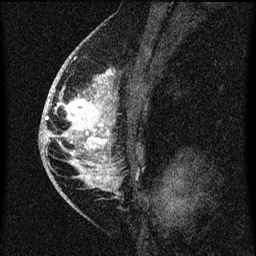
Breast MRI (dynamic contrast-enhanced), one sagittal slice; slice 39 of 60 in the series (ordered by position); dynamic contrast-enhanced series, image 2 of 3 at this slice position (ordered by acquisition); 1.5 T; TE 4.2 ms, TR 8 ms; 2 mm slice thickness; 256 × 256 image matrix, field of view 180 × 180 mm. Patient: female, 46 years.
Outlined on this slice (semi-automatically segmented with operator editing):
- analysis volume of interest (the breast-tissue region the enhancement analysis was run in; not a lesion): box from (x=51, y=68) to (x=117, y=195) px
- tumour enhancement mask (voxels above the 70 % enhancement threshold inside the analysis volume of interest): (x=51, y=68)–(x=116, y=191)